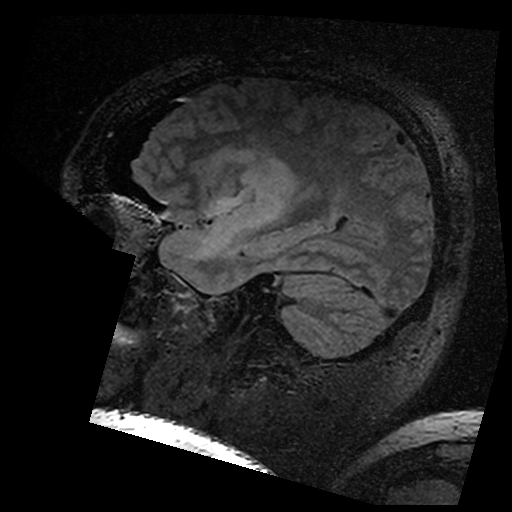
Brain MRI from a brain-tumour surgery series, one sagittal slice. Slice 121 of 176 in the series (ordered by position). T2 FLAIR. 512 × 512 image matrix. Case-level facts recorded for this patient, not image findings: histopathology: Astrocytoma; WHO grade: 3; IDH mutation: yes; tumour location: Left Insular.
Outlined on this slice (expert manual segmentation):
- residual tumour: bounding box (x1, y1, x2, y2) in pixels: (211, 145, 292, 201)